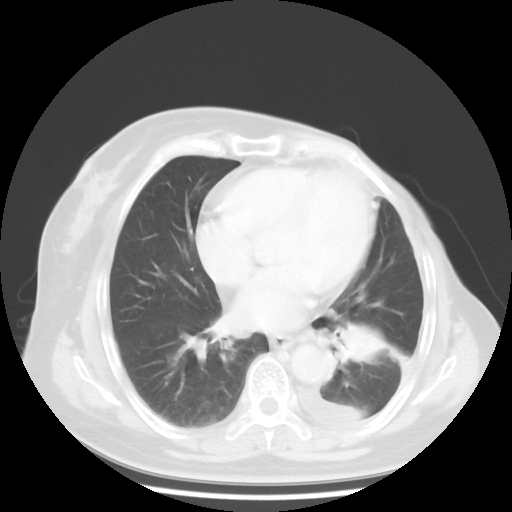
Chest CT, one axial slice. Slice 20 of 48 in the series (ordered by position). 120 kVp. Lung window (W 1500 / L -600 HU). 5 mm slice thickness. 512 × 512 image matrix, field of view 360 × 360 mm. Patient: female, 63 years. From the clinical record (not read from this slice): clinical TNM (as recorded): T2 N0 M1.
Structures marked on this image (bounding box drawn by a radiologist):
- lung tumour (recorded histology: adenocarcinoma): bounding box [x1, y1, x2, y2] px = [333, 315, 385, 368]